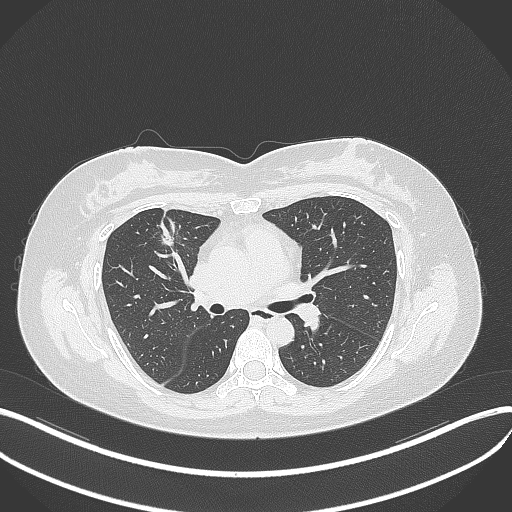
Chest CT, one axial slice. Slice 189 of 273 in the series (ordered by position). Reconstruction kernel B70f. 120 kVp. Lung window (W 1500 / L -600 HU). 1 mm slice thickness. 512 × 512 image matrix, field of view 400 × 400 mm. Female patient, age 42 years. Case-level facts recorded for this patient, not image findings: clinical TNM (as recorded): T1b N0 M0.
Outlined on this slice (bounding box drawn by a radiologist):
- lung tumour (recorded histology: adenocarcinoma): bounding box (x1, y1, x2, y2) in pixels: (154, 225, 179, 250)